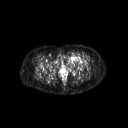
FDG PET of an extremity soft-tissue mass (from a PET/CT study), one axial slice; slice 44 of 267 in the series (ordered by position); 128 × 128 image matrix. Female patient, age 47 years. Case-level facts recorded for this patient, not image findings: histological type: myxofibrosarcoma; grade: intermediate; site of the primary tumour: left thigh.
Annotated regions visible in this slice (expert contour drawn on MRI and transferred to this co-registered scan by the dataset authors):
- gross tumour volume including surrounding oedema: bounding box <65,54,84,64> (left, top, right, bottom; pixels)
- gross tumour volume (mass): <69,54,78,61>